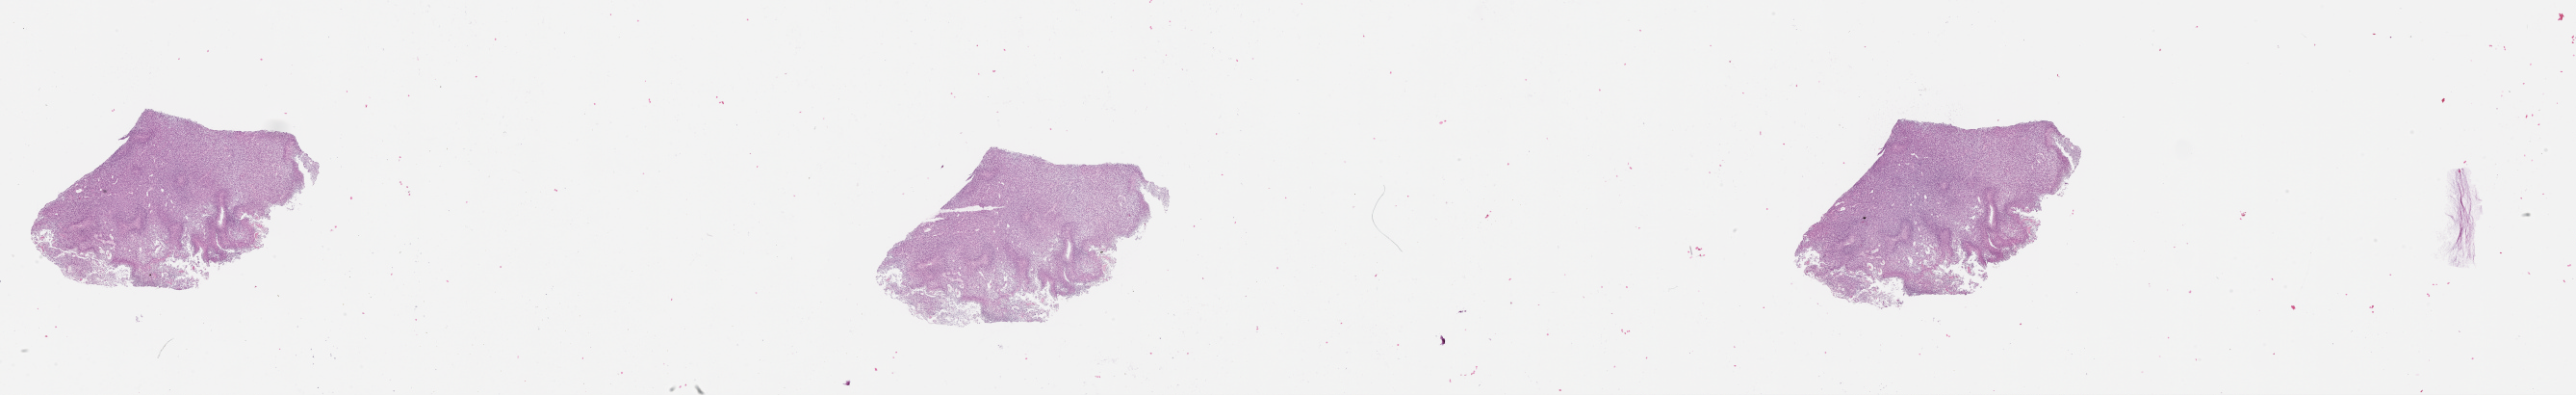
H&E-stained whole-slide image, low-resolution overview of the scanned area, about 43.1 x 6.6 mm (acquisition: 20x scan); brain, tumour tissue. Female, 80 y/o.
Diagnosis: Glioblastoma.